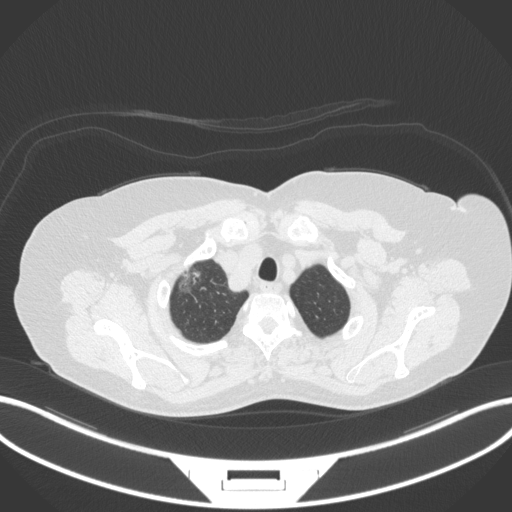
Chest CT, one axial slice. Position 315 of 365 along the scan axis. Reconstruction kernel B31f. 120 kVp. Lung window (W 1500 / L -600 HU). 1 mm slice thickness. 512 × 512 image matrix, field of view 400 × 400 mm. Patient: female, 62 years. From the clinical record (not read from this slice): clinical TNM (as recorded): T1c N0 M0.
Annotated regions visible in this slice (bounding box drawn by a radiologist):
- lung tumour (recorded histology: adenocarcinoma): bounding box [x1, y1, x2, y2] px = [176, 260, 208, 296]